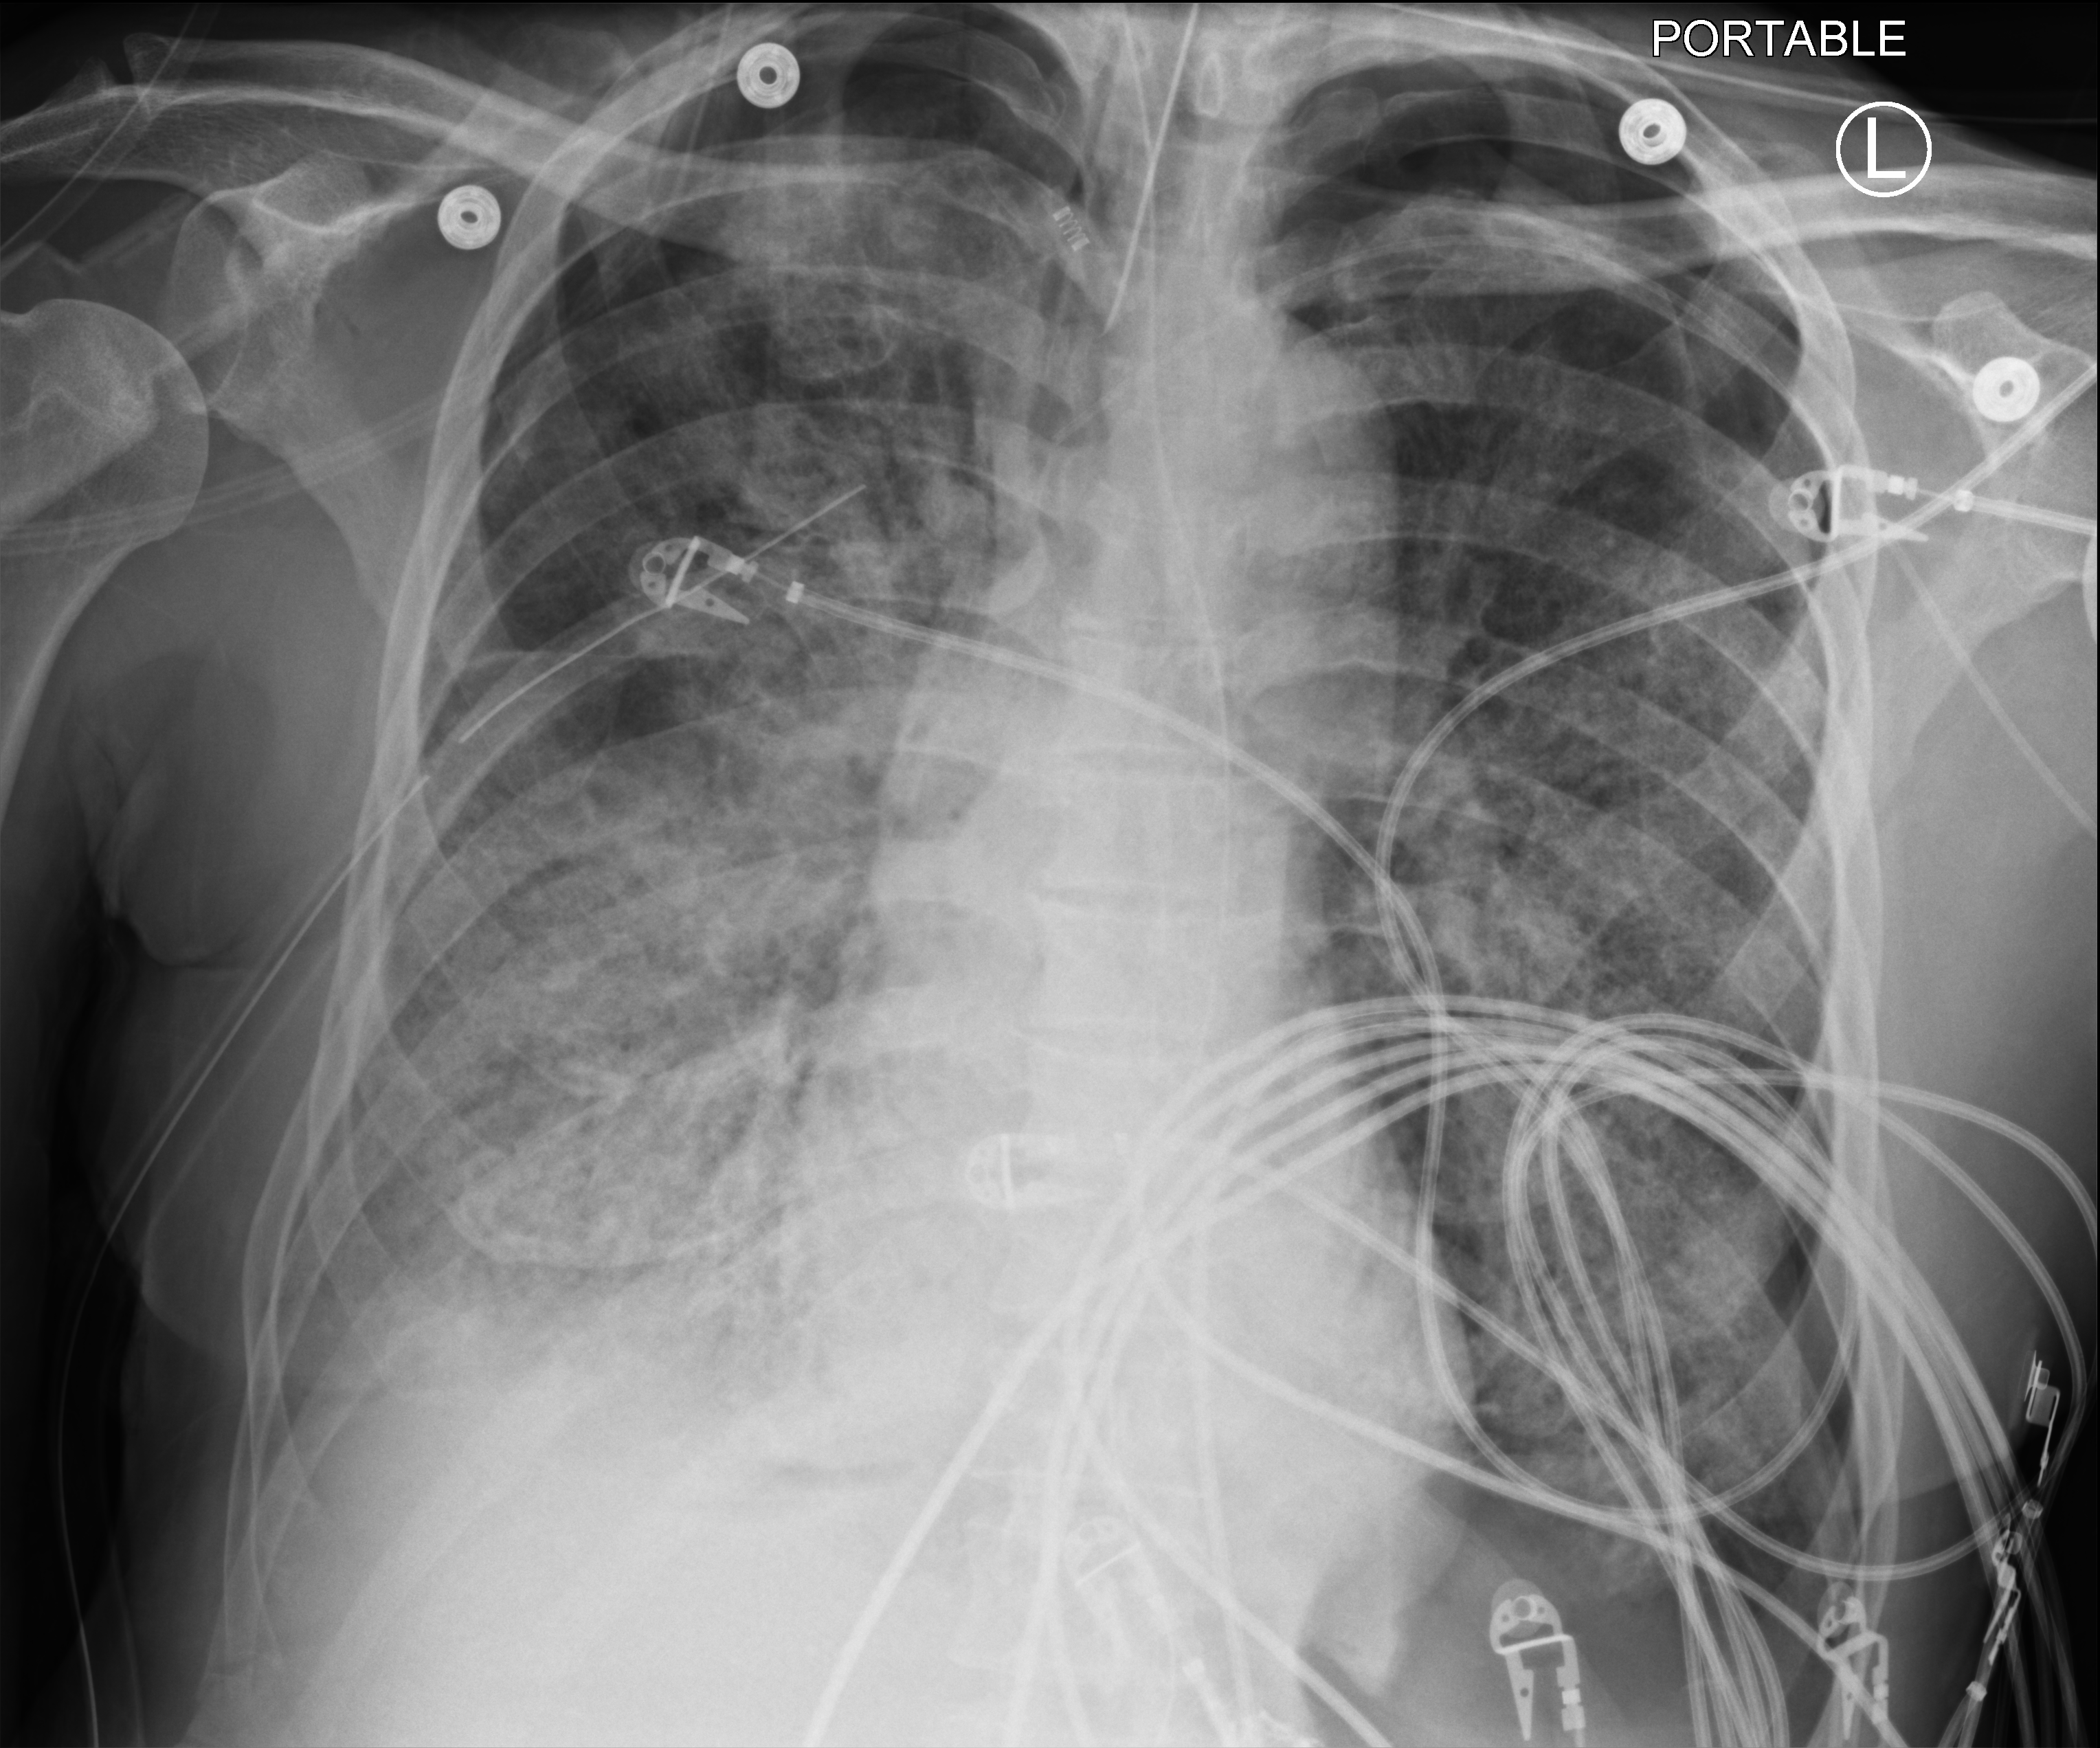
Bedside chest radiograph (computed radiography), anteroposterior (AP) projection. Male patient hospitalised with COVID-19, age 60–74 years.
From the hospital-stay record, not from the radiograph (when in the stay this image was taken is not recorded): mechanically ventilated during this hospital stay: yes; smoking status (admission record): former; admitted to intensive care during this hospital stay: yes.